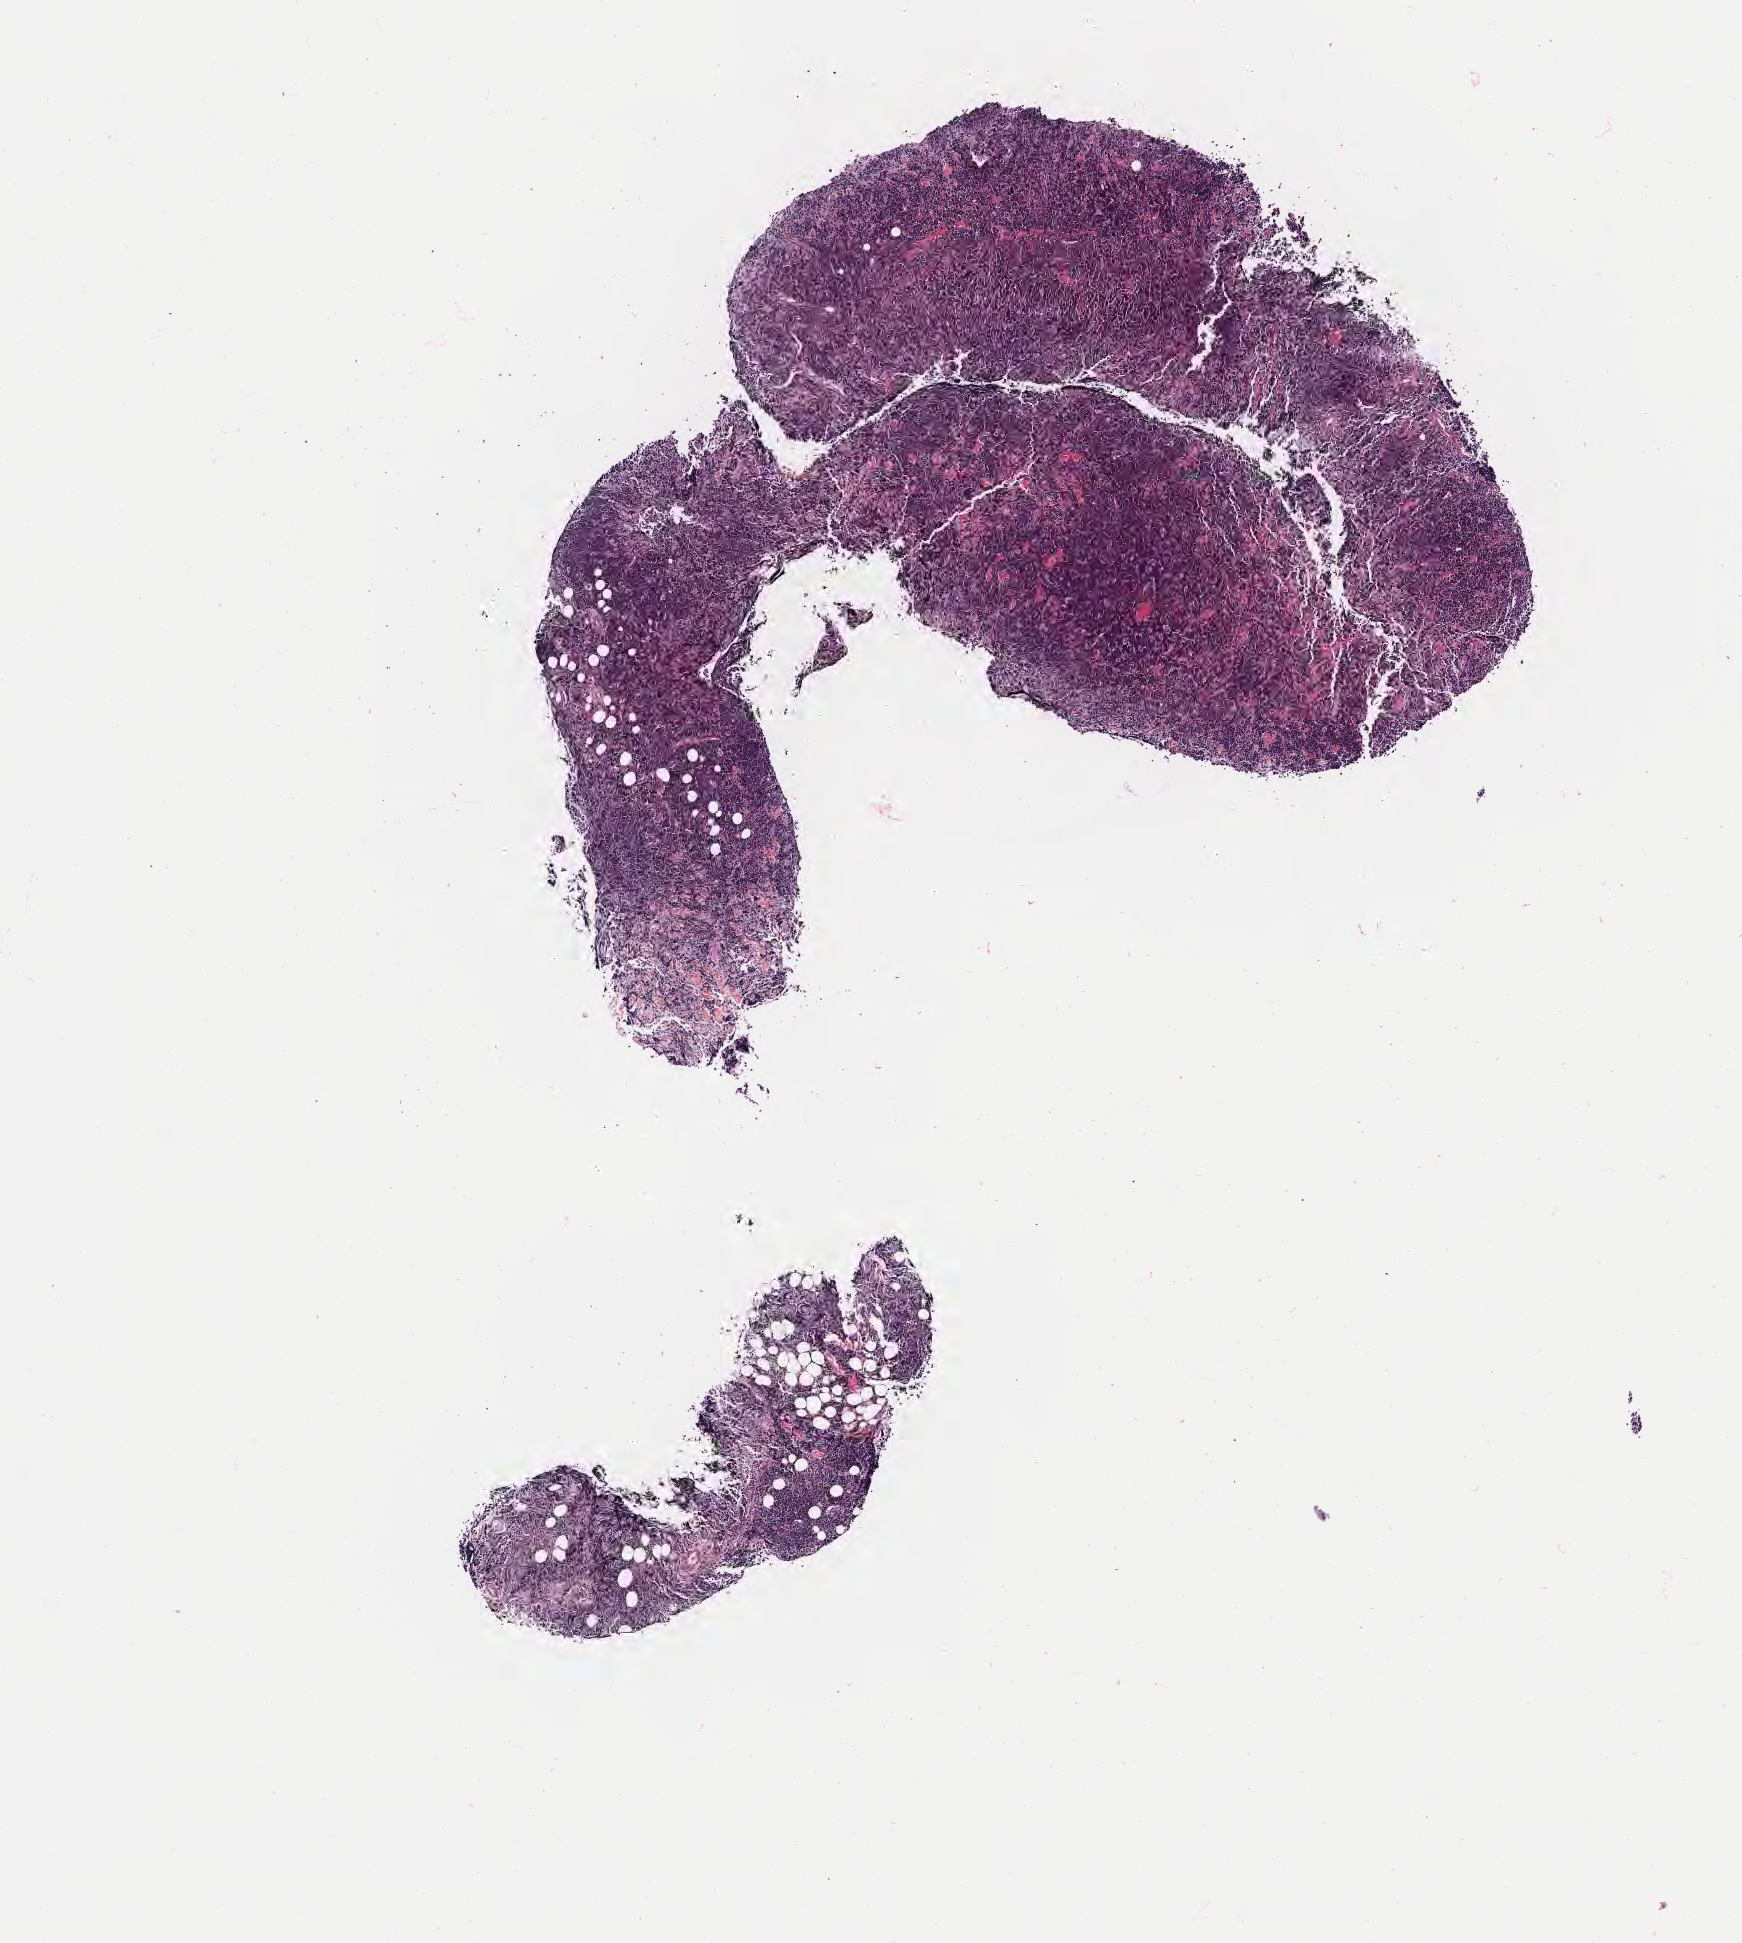
Hematoxylin and eosin (H&E) whole-slide image — low-resolution overview of the scanned area, about 7.0 x 7.9 mm. Tumor tissue. Anatomic site: head and neck. Female patient, 55 years old.
Histologic diagnosis: Burkitt lymphoma, NOS.